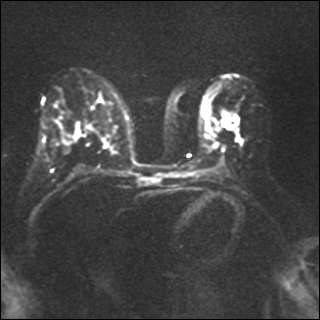
Breast MRI, one axial slice; diffusion-weighted series; image 2 of 4 stored at this slice position (different b-values; order by instance number); 1.5 T; 320 × 320 image matrix, field of view 320 × 320 mm. Female patient.
Structures marked on this image (manually delineated by an expert):
- tumour on diffusion-weighted imaging: bounding box [x1, y1, x2, y2] px = [223, 114, 232, 129]